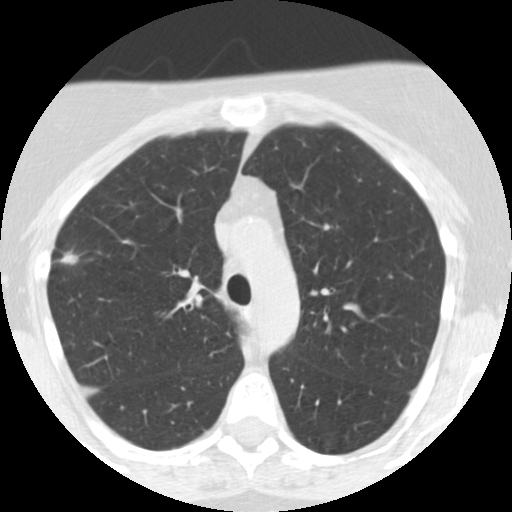
Low-dose screening chest CT, one axial slice; position 178 of 248 along the scan axis; reconstruction kernel STANDARD; 120 kVp; lung window (W 1500 / L -600 HU); 2.5 mm slice thickness; 512 × 512 image matrix, field of view 287 × 287 mm.
Outlined on this slice (expert manual segmentation):
- lesion 1 (tumor, upper lobe of right lung): bounding box (x1, y1, x2, y2) in pixels: (61, 254, 77, 263)